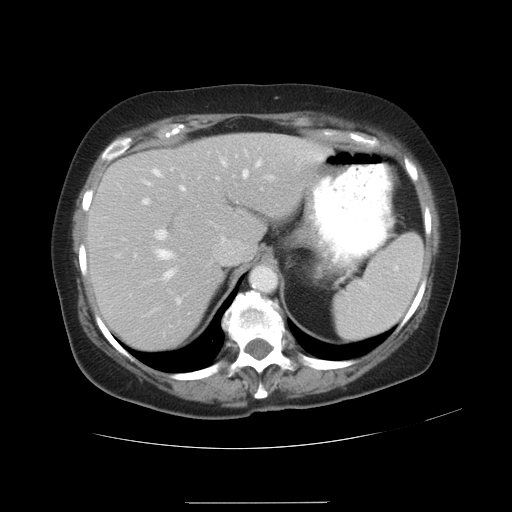
Contrast-enhanced abdominal CT, one axial slice. Slice 22 of 32 in the series (ordered by position). Reconstruction kernel STANDARD. 120 kVp. Intravenous contrast given. Soft-tissue window (W 400 / L 40 HU). 7.5 mm slice thickness. 512 × 512 image matrix. Female patient, age 65 years. From the clinical record (not read from this slice): diagnosis: colorectal cancer liver metastases, imaged before liver resection.
Outlined on this slice (expert manual segmentation):
- hepatic veins: bounding box [x1, y1, x2, y2] px = [156, 160, 261, 305]
- liver: [90, 134, 324, 349]
- planned liver remnant (the part of the liver to remain after resection): [90, 140, 237, 349]
- portal vein (with intrahepatic branches): [152, 154, 238, 241]
- liver metastasis: [266, 162, 271, 168]